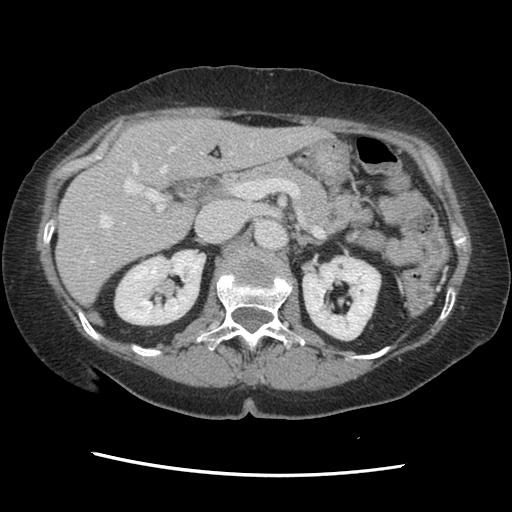
Contrast-enhanced abdominal CT, one axial slice; position 80 of 141 along the scan axis; soft-tissue window (W 400 / L 40 HU); 2.5 mm slice thickness; 512 × 512 image matrix, field of view 330 × 330 mm. Female patient, age 61 years. Case-level facts recorded for this patient, not image findings: diagnosis: colorectal cancer liver metastases, imaged before liver resection; multiple liver metastases: no; largest metastasis: 2.4 cm.
Outlined on this slice (expert manual segmentation):
- hepatic veins: bounding box <90,140,289,263> (left, top, right, bottom; pixels)
- liver: <57,119,321,303>
- planned liver remnant (the part of the liver to remain after resection): <57,119,321,303>
- portal vein (with intrahepatic branches): <90,161,164,211>